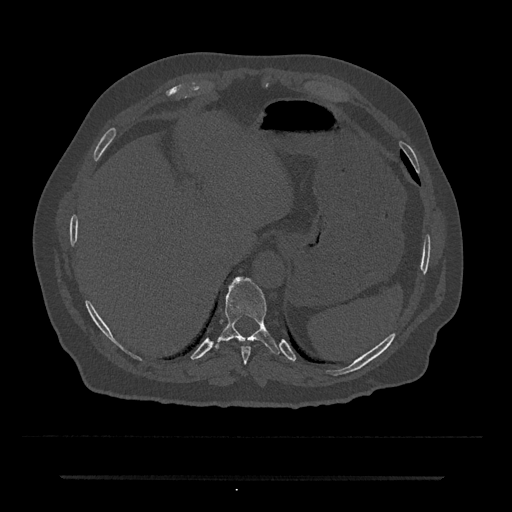
CT including the spine, one axial slice. Slice 240 of 797 in the series (ordered by position). Reconstruction kernel Br40s/3. 120 kVp. Bone window (W 1800 / L 400 HU). 0.5 mm slice thickness. 512 × 512 image matrix. Male patient, age 69 years. From the clinical record (not read from this slice): primary cancer: prostate.
Outlined on this slice (semi-automatic segmentation, software-assisted and operator-edited):
- T10 vertebra: bounding box [x1, y1, x2, y2] px = [214, 276, 280, 355]
- T9 vertebra: [241, 346, 251, 364]